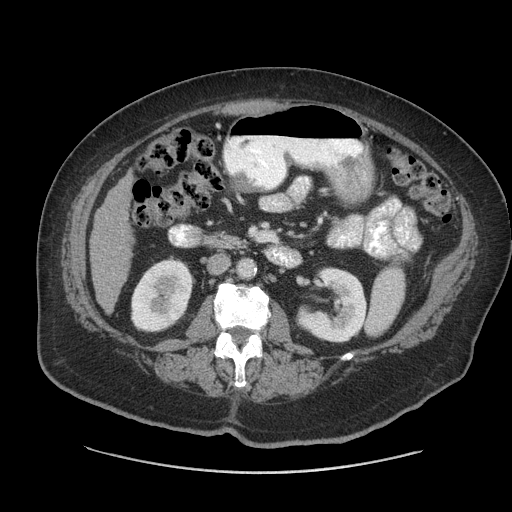
Contrast-enhanced abdominal CT (liver protocol), one axial slice; position 18 of 91 along the scan axis; 140 kVp; soft-tissue window (W 400 / L 40 HU); 2.5 mm slice thickness; 512 × 512 image matrix, field of view 420 × 420 mm. From the clinical record (not read from this slice): diagnosis: hepatocellular carcinoma (patient treated with transarterial chemoembolisation; whether this scan precedes or follows treatment is not stated here); TNM stage (as recorded): Stage-I; Child-Pugh class: A; tumour differentiation: well differentiated.
Annotated regions visible in this slice (semi-automatic segmentation, software-assisted and operator-edited):
- liver parenchyma outside the tumour (the mass and vessels are separate outlines, so this box may not span the whole liver): bounding box <90,173,134,312> (left, top, right, bottom; pixels)